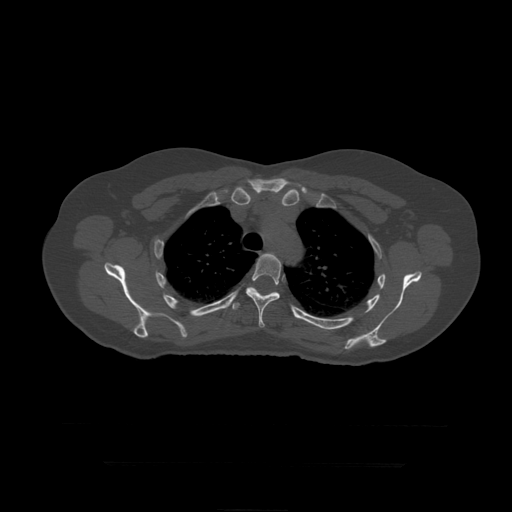
CT including the spine, one axial slice. Position 334 of 399 along the scan axis. 120 kVp. Bone window (W 1800 / L 400 HU). 1.25 mm slice thickness. 512 × 512 image matrix, field of view 450 × 450 mm. Patient age 41 years. From the clinical record (not read from this slice): primary cancer: breast.
Annotated regions visible in this slice (semi-automatically segmented with operator editing):
- T5 vertebra: bounding box [x1, y1, x2, y2] px = [246, 253, 282, 328]
- T6 vertebra: [231, 287, 277, 310]